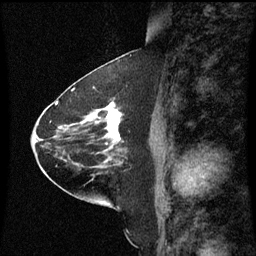
Breast MRI (dynamic contrast-enhanced), one sagittal slice; dynamic contrast-enhanced series, image 2 of 3 at this slice position (ordered by acquisition); 1.5 T; TE 4.2 ms, TR 8.9 ms; 2 mm slice thickness; 256 × 256 image matrix, field of view 200 × 200 mm. Patient: female, 63 years. Case-level facts recorded for this patient, not image findings: setting: breast cancer imaged before/during neoadjuvant chemotherapy; receptor status: HR-positive, HER2-negative.
Structures marked on this image (semi-automatic segmentation, software-assisted and operator-edited):
- analysis volume of interest (the breast-tissue region the enhancement analysis was run in; not a lesion): bounding box (x1, y1, x2, y2) in pixels: (77, 100, 124, 151)
- tumour enhancement mask (voxels above the 70 % enhancement threshold inside the analysis volume of interest): (103, 102, 120, 141)